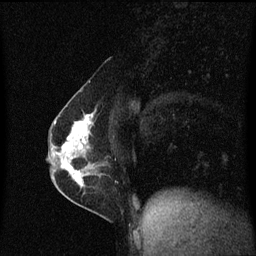
Breast MRI (dynamic contrast-enhanced), one sagittal slice. Position 28 of 60 along the scan axis. Dynamic contrast-enhanced series, image 2 of 3 at this slice position (ordered by acquisition). 1.5 T. TE 4.2 ms, TR 8.4 ms. 2 mm slice thickness. 256 × 256 image matrix, field of view 200 × 200 mm. Patient: female, 40 years.
Structures marked on this image (semi-automatically segmented with operator editing):
- analysis volume of interest (the breast-tissue region the enhancement analysis was run in; not a lesion): bounding box <57,110,105,191> (left, top, right, bottom; pixels)
- tumour enhancement mask (voxels above the 70 % enhancement threshold inside the analysis volume of interest): <61,114,93,187>